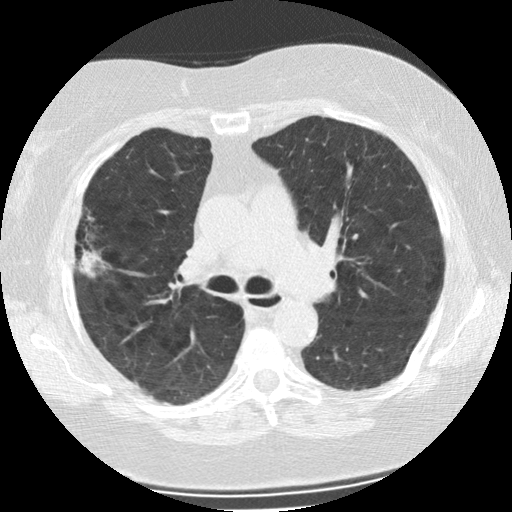
Chest CT (low-dose screening protocol), one axial image; second annual screen; lung window (W 1500 / L -600 HU); 120 kVp; slice 81 of 225 in the series; 512 × 512 image matrix, field of view 320 × 320 mm. Female, age 73 years at enrolment.
• Expert reader's lesion annotation, bounding box (x1, y1, x2, y2) in pixels: (54, 217, 112, 287).
• The screening reader recorded 2 non-calcified nodules or masses ≥4 mm on this exam (right upper lobe, left upper lobe); which of them this box marks is not recorded.
• Later outcome: lung cancer diagnosed 47 days after this screen — bronchiolo-alveolar adenocarcinoma, NOS, right upper lobe, moderately differentiated (G2), stage IIIB (AJCC 6th edition), 21 mm at pathology.